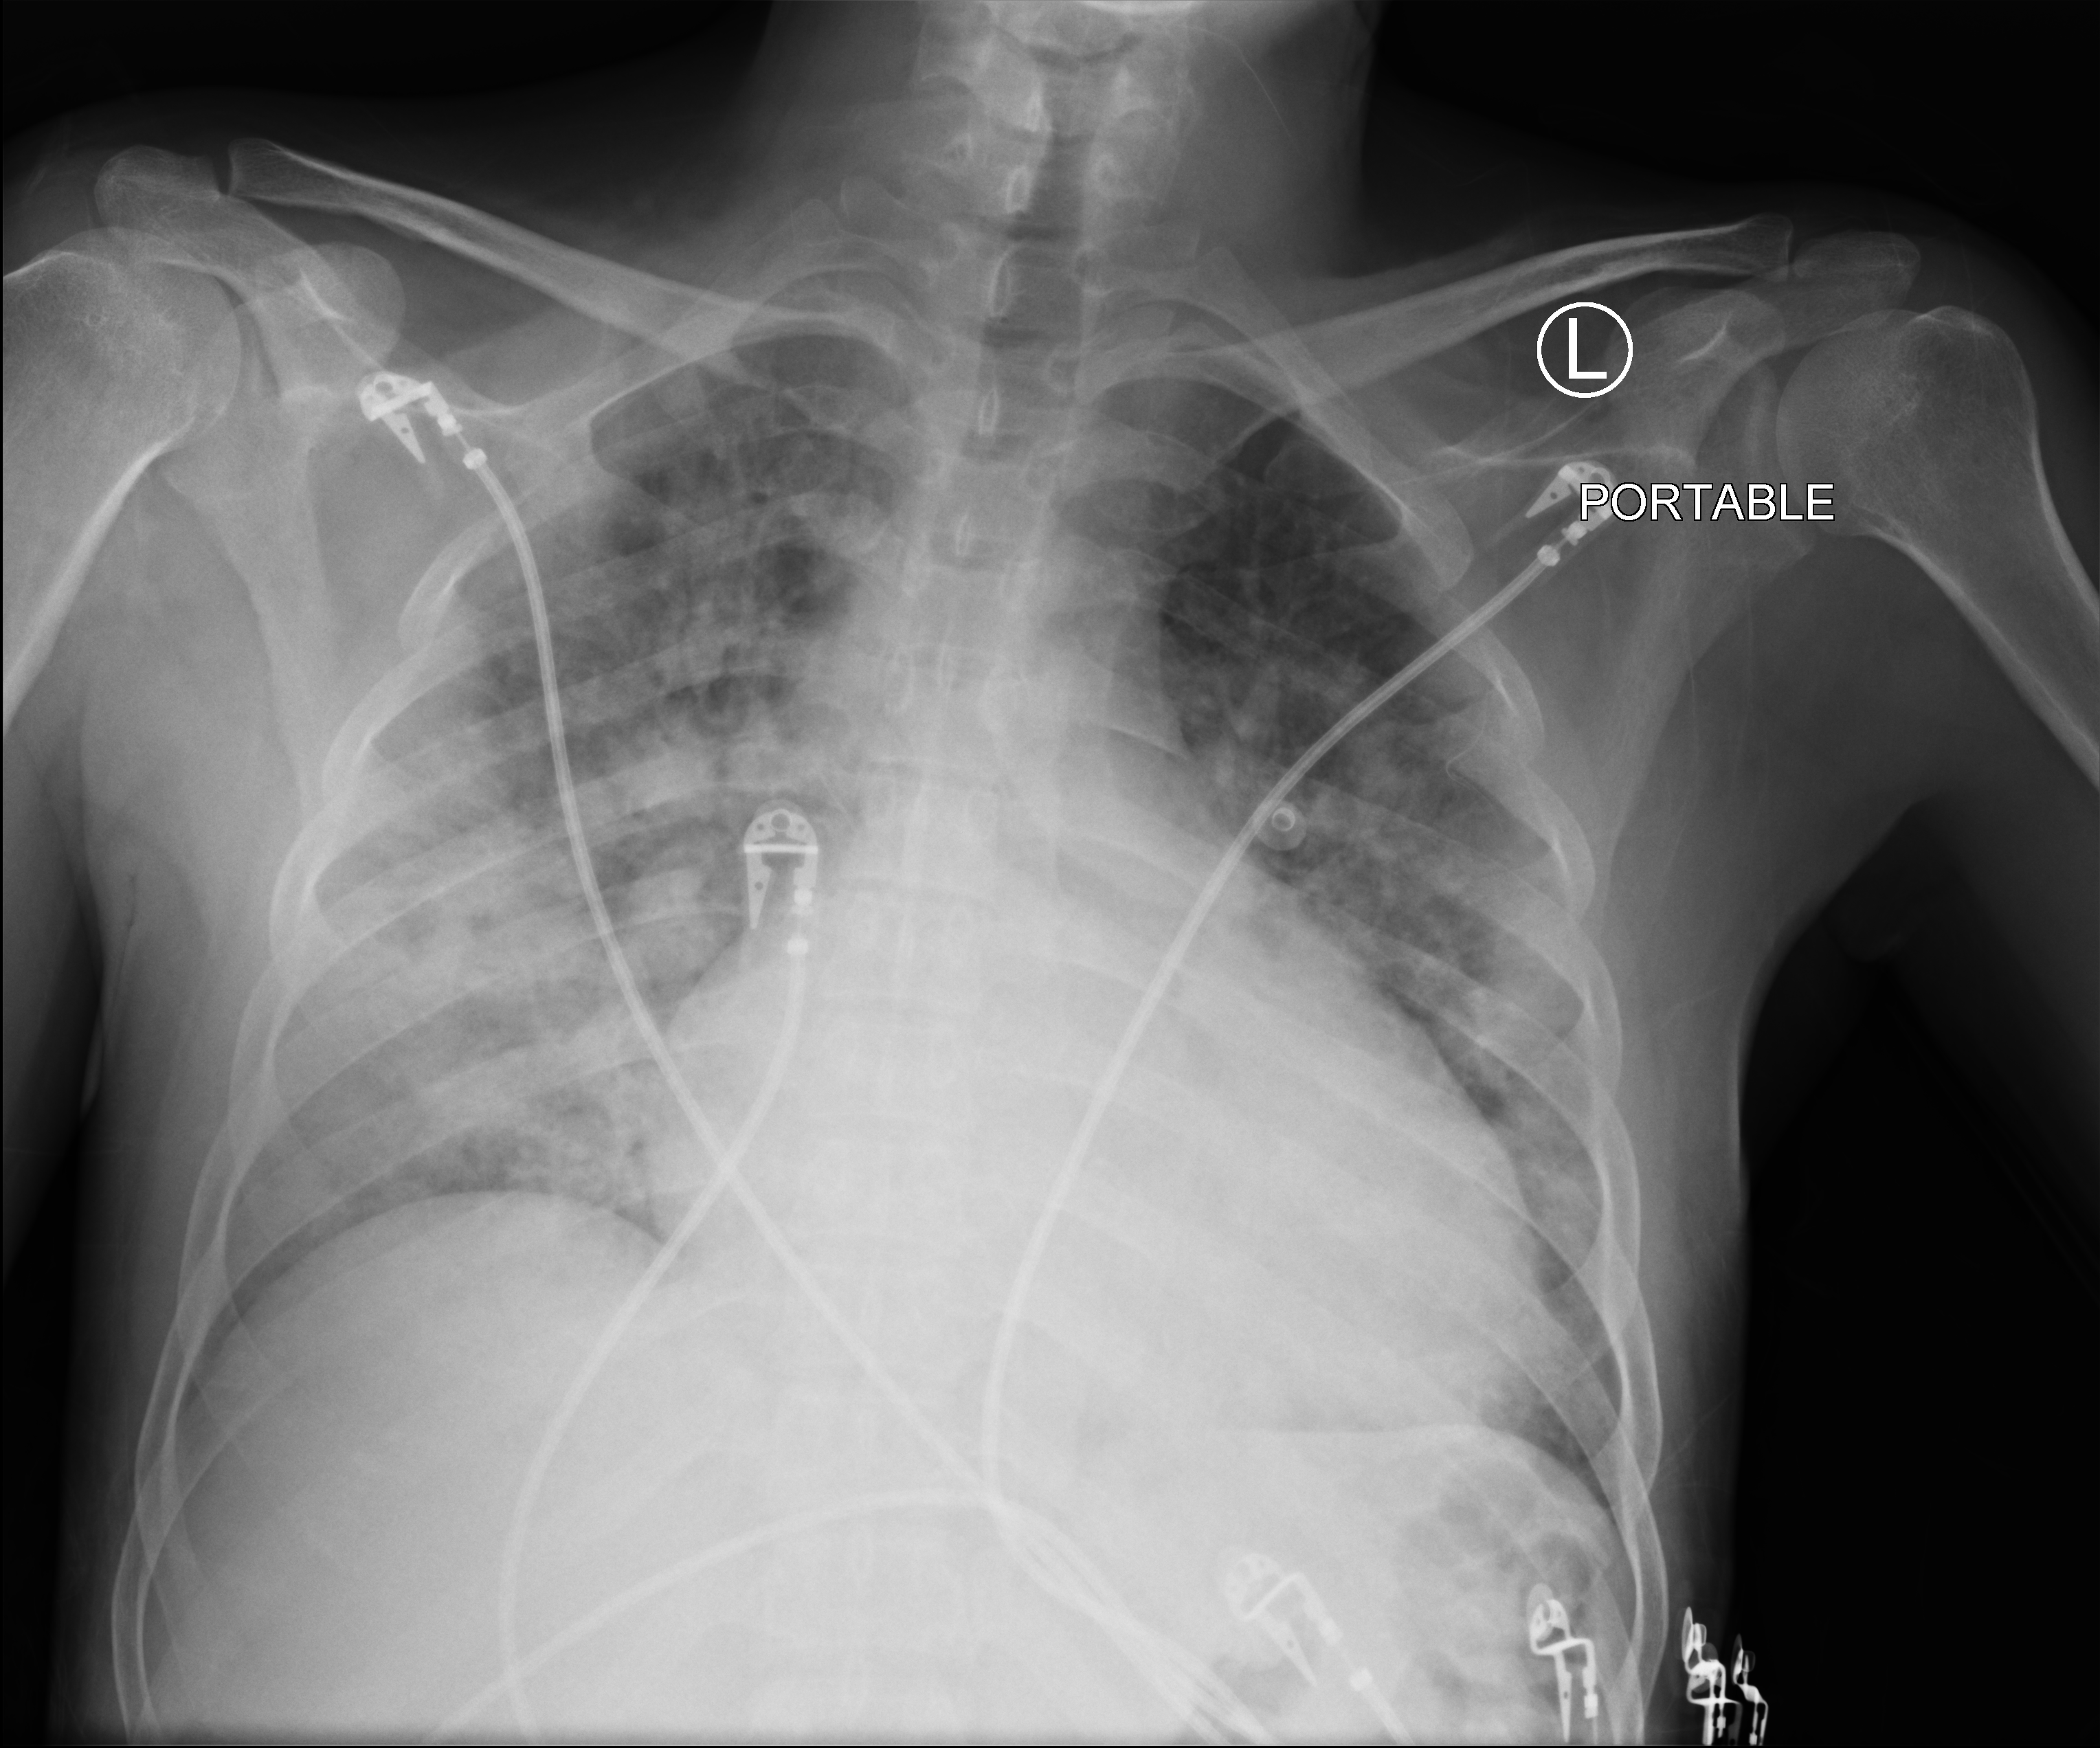
Bedside chest radiograph (computed radiography); anteroposterior (AP) projection. Patient hospitalised with COVID-19; male, aged 18–59 years.
From the hospital-stay record, not from the radiograph (when in the stay this image was taken is not recorded):
- admitted to intensive care during this hospital stay: no
- hypertension (admission record): yes
- COPD (admission record): no